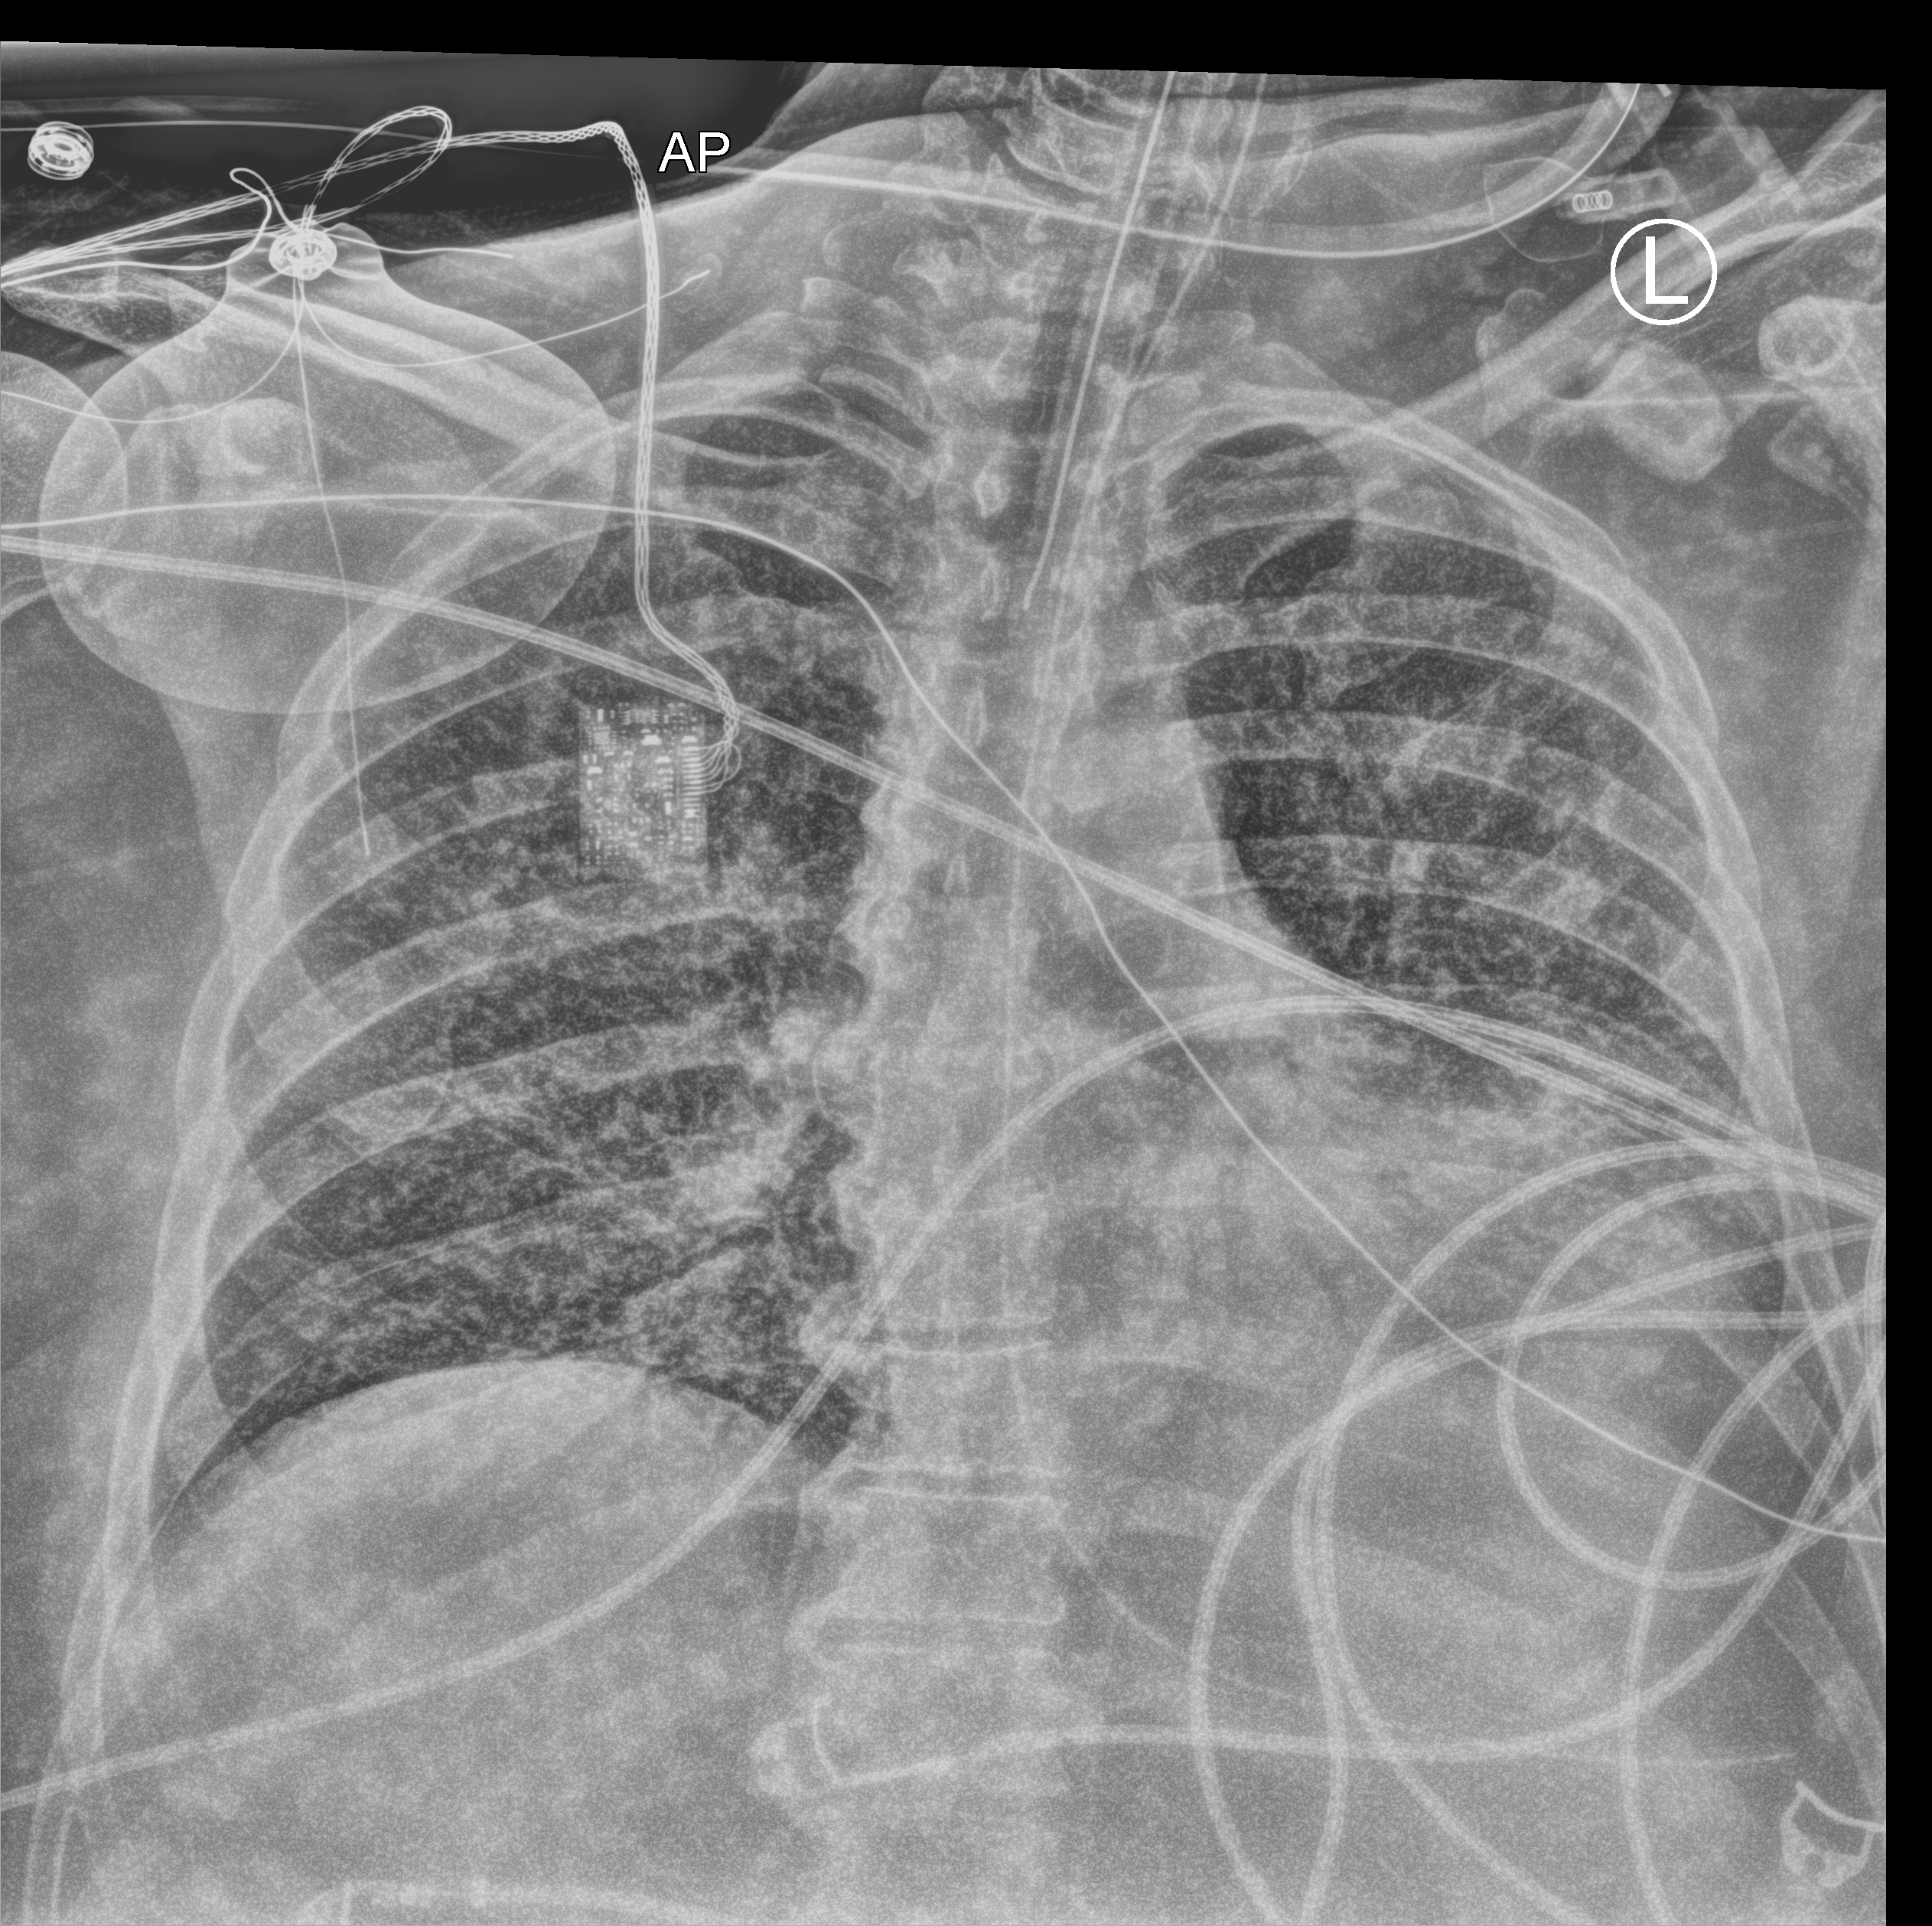
Chest X-ray (portable). Adult patient hospitalised with COVID-19, age 18–59 years.
Admission-level facts for this patient (not findings on this image; timing relative to this image not recorded): admitted to intensive care during this hospital stay: yes.